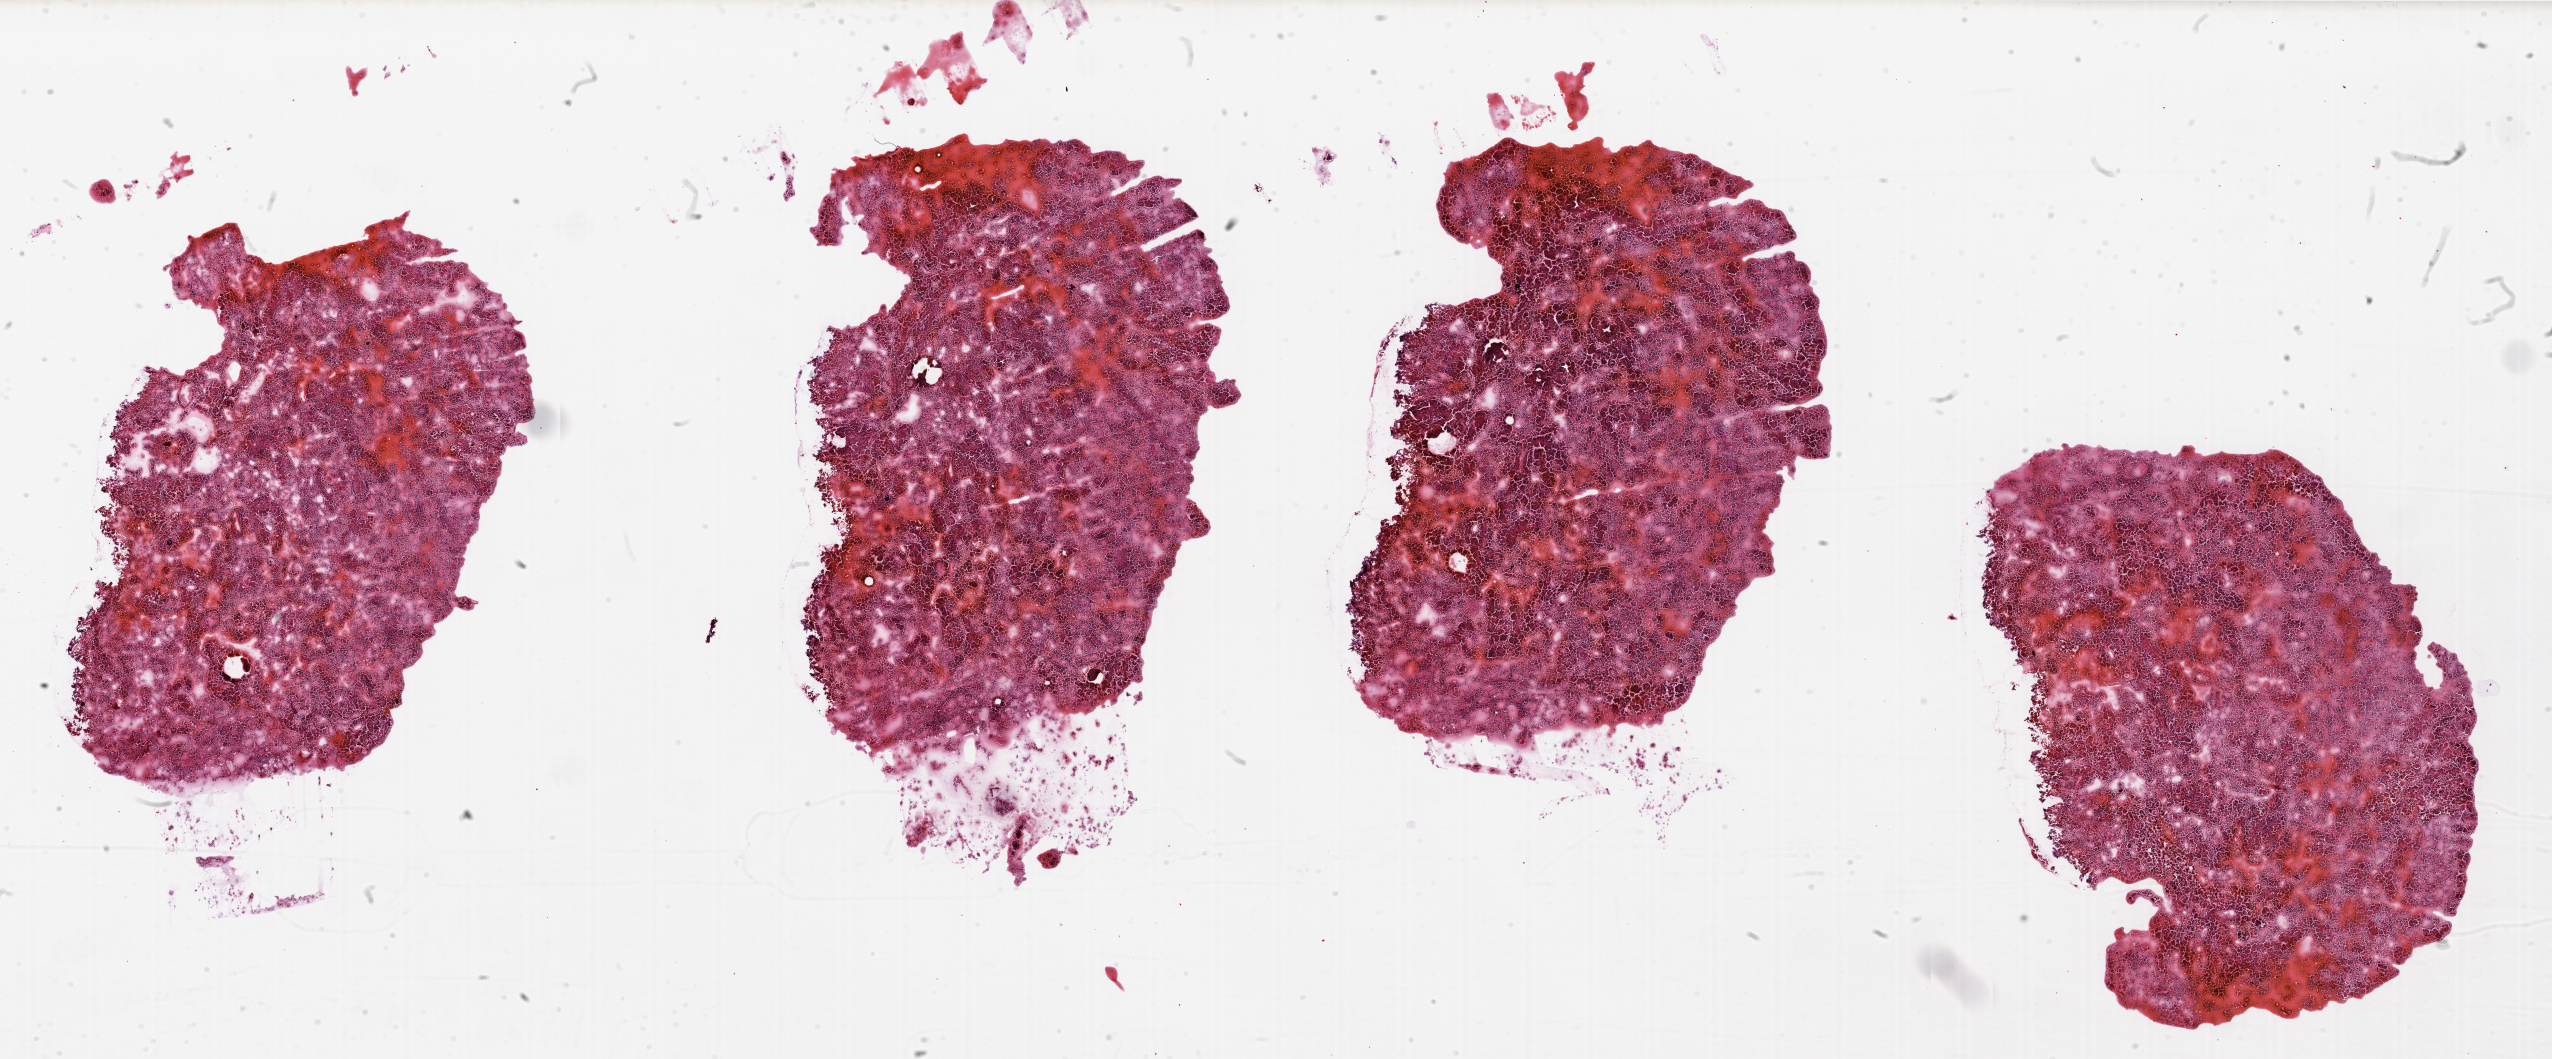
H&E whole-slide image — whole scanned area (about 40.4 x 16.7 mm, slide scanned at 20x) shown as a low-resolution overview; tumour tissue sample, kidney. Female, 31 y/o. Histologic grade: G2 (moderately differentiated).
AJCC pathologic stage: I. Primary tumour site (as recorded): middle. Diagnosis: Renal cell carcinoma, NOS.